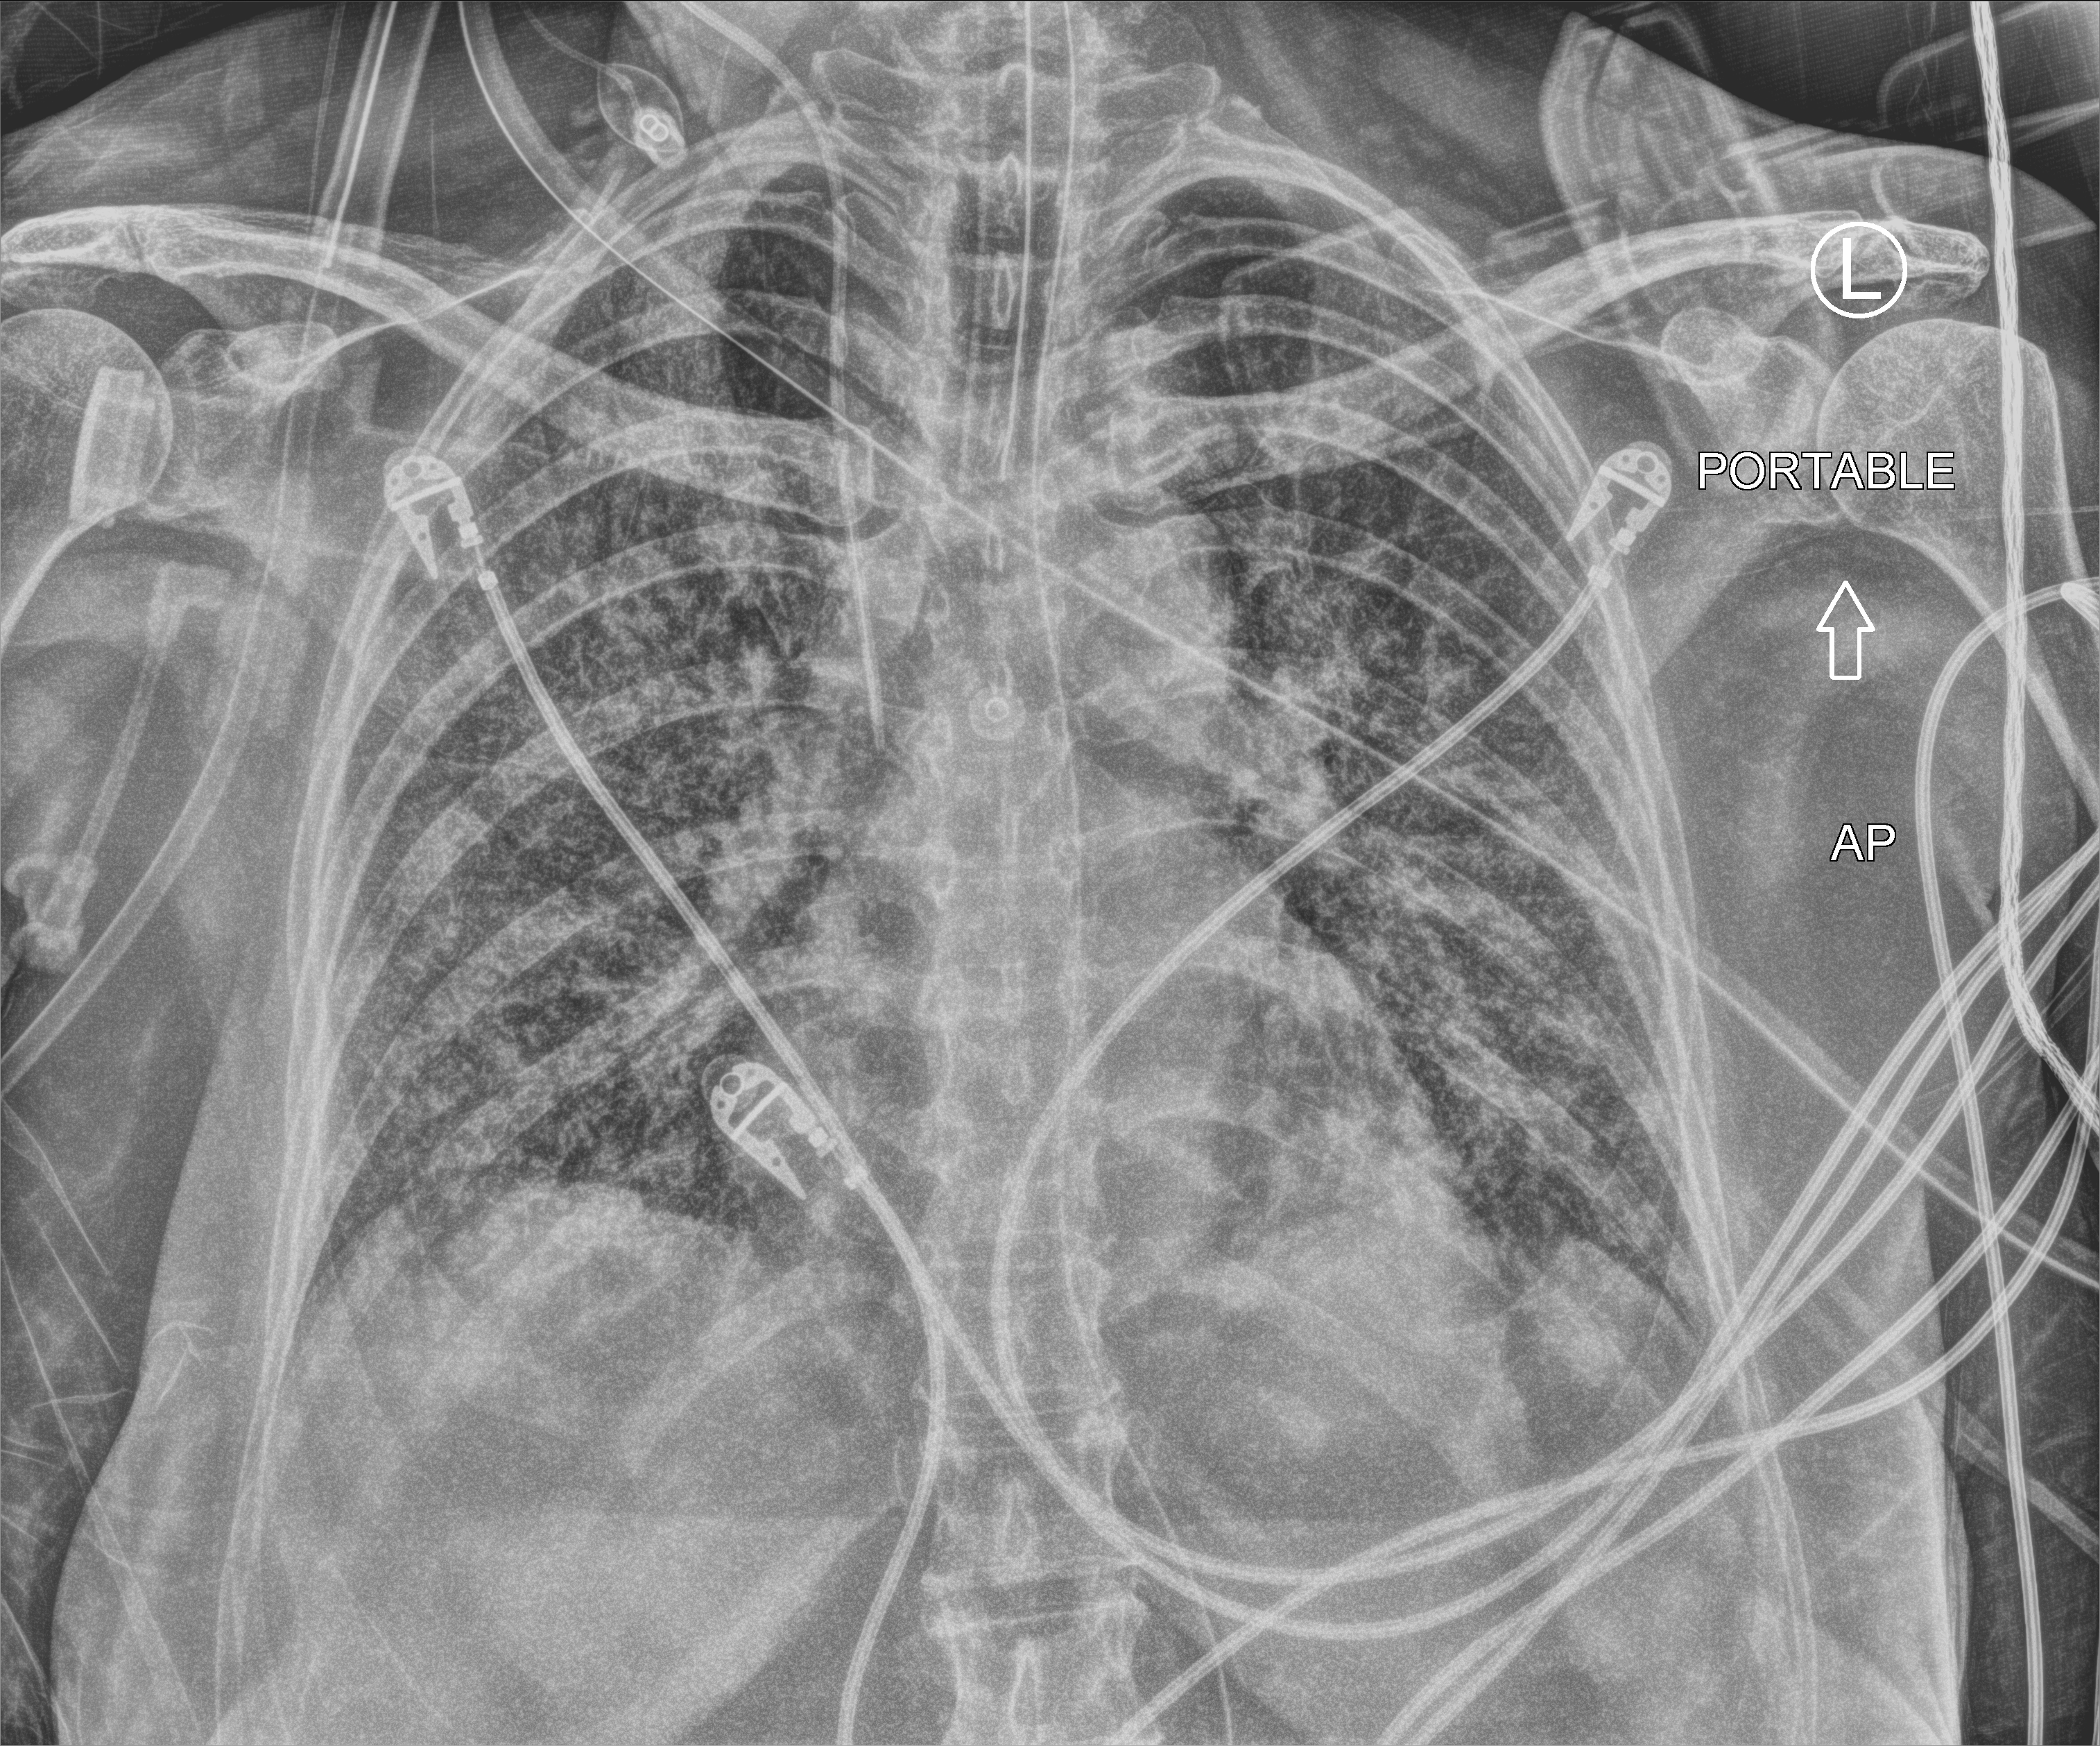
Chest X-ray (portable), anteroposterior (AP) projection. Female patient hospitalised with COVID-19, age 60–74 years.
From the hospital-stay record, not from the radiograph (when in the stay this image was taken is not recorded):
- other chronic lung disease (admission record): no